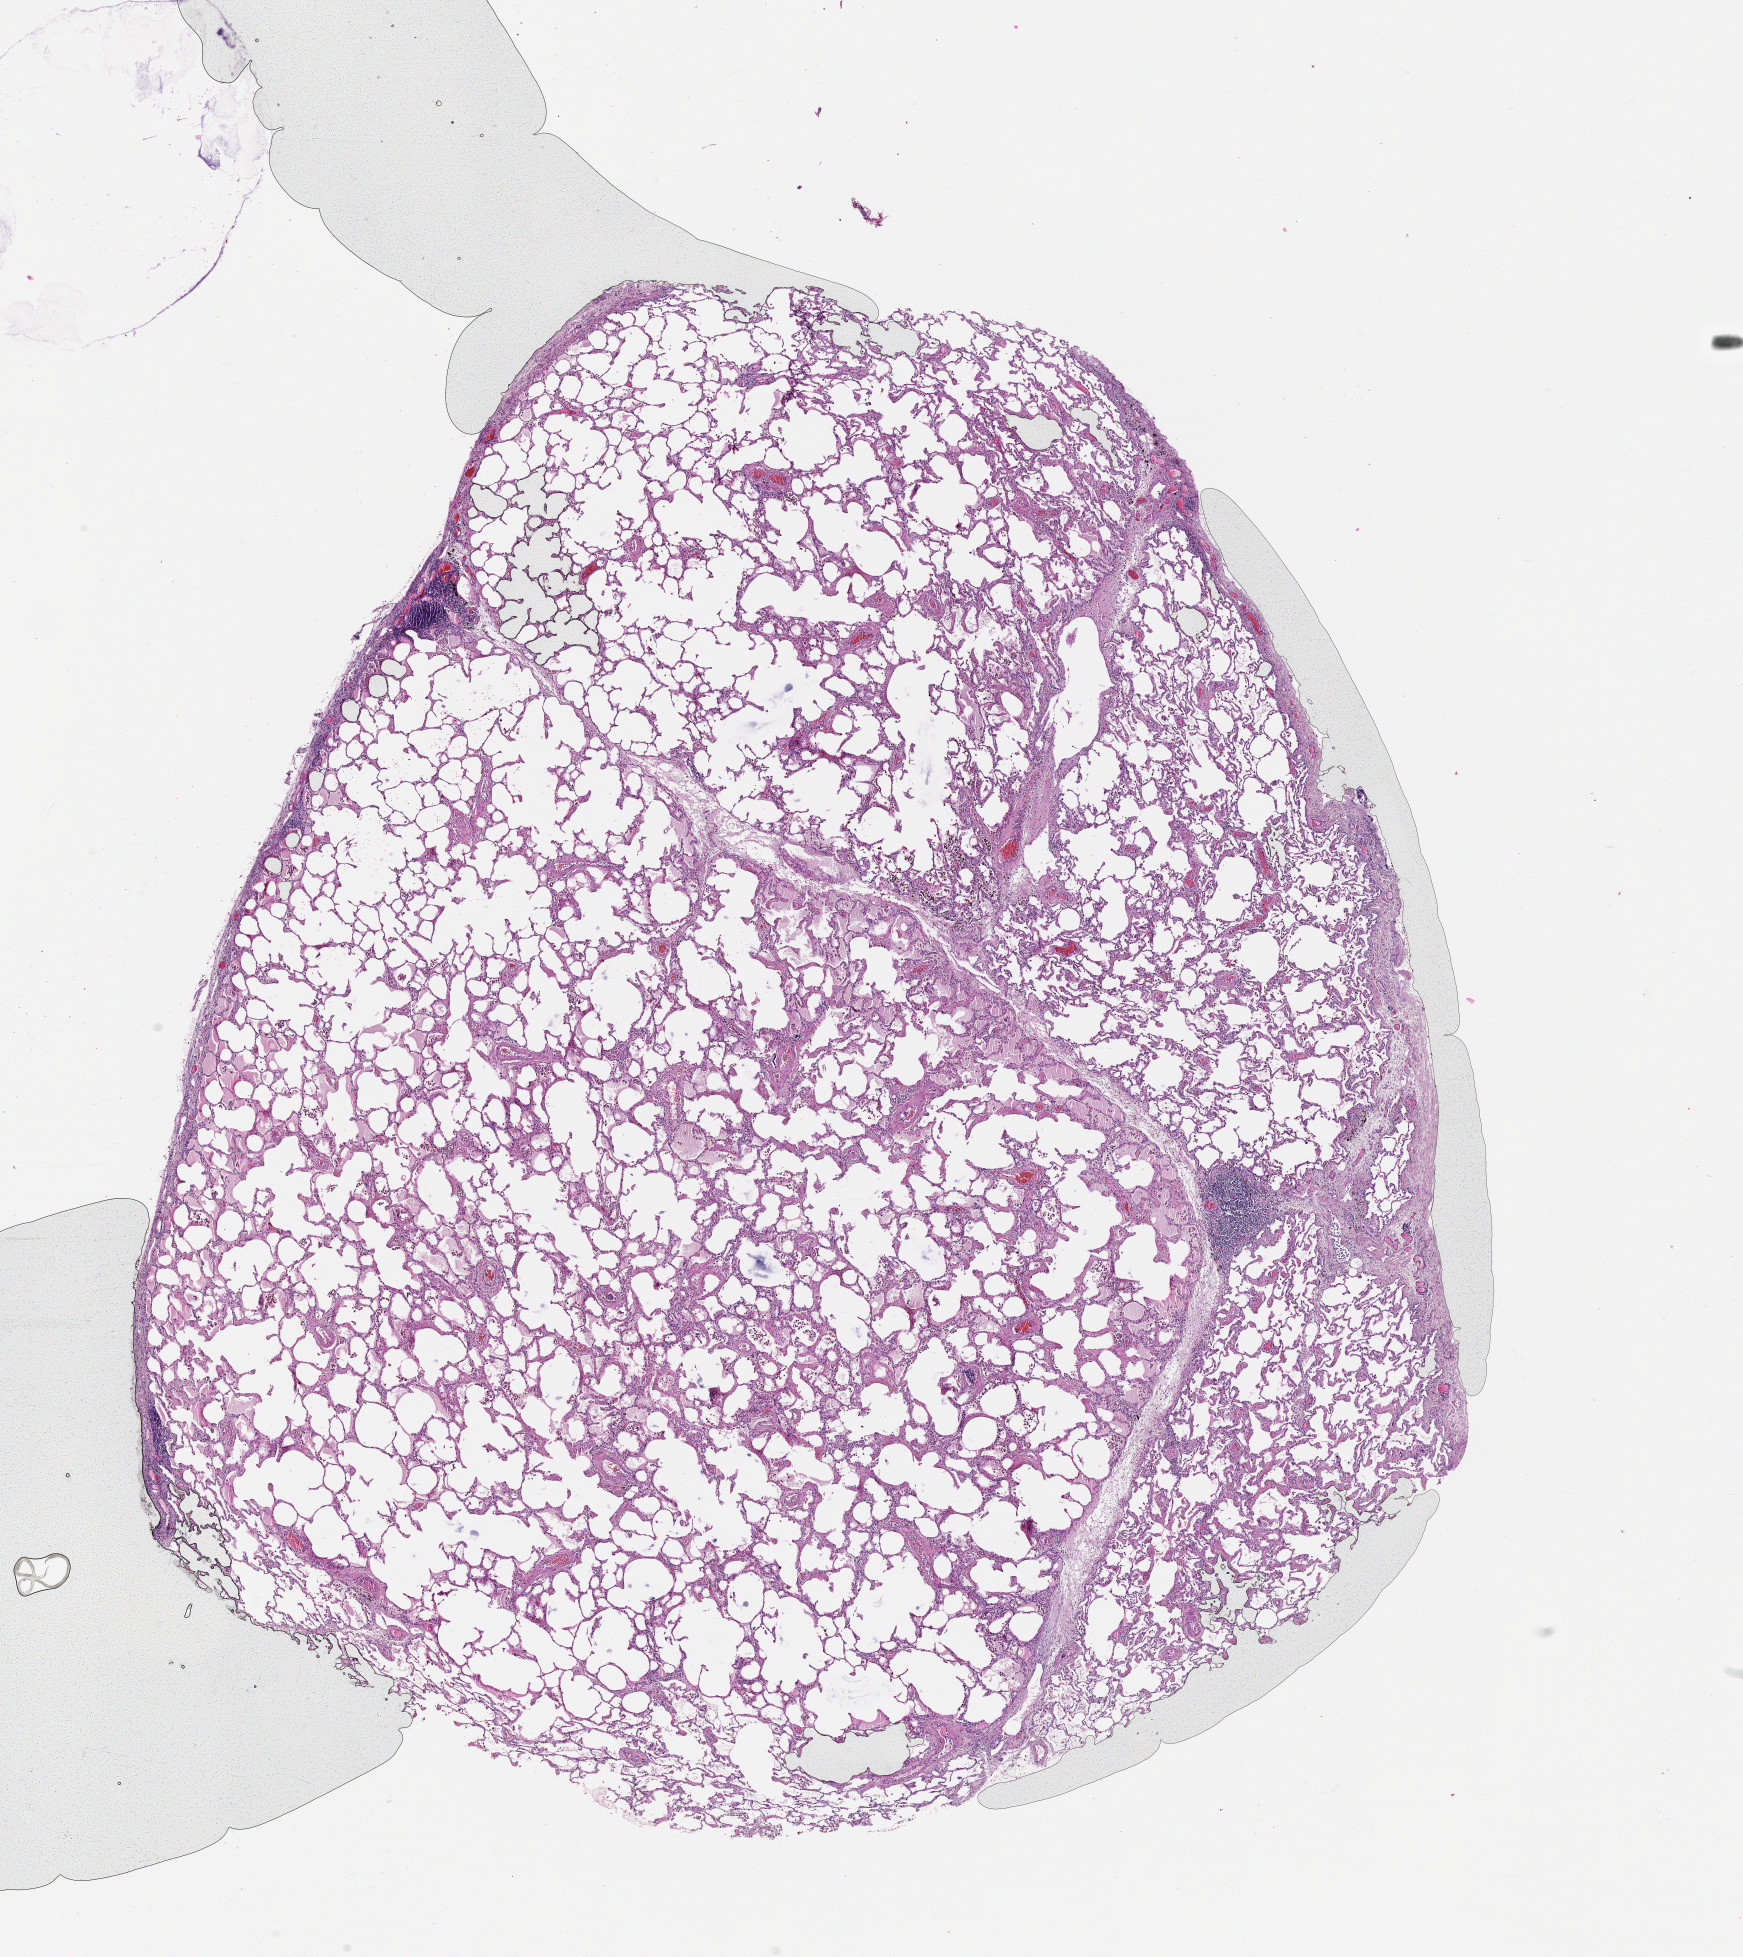
Whole-slide histology image, H&E, low-resolution overview of the scanned area, about 14.0 x 15.8 mm (slide scanned at 20x). Lung, tissue type not recorded.
Patient diagnosis (cohort enrolment): squamous cell carcinoma (lung).